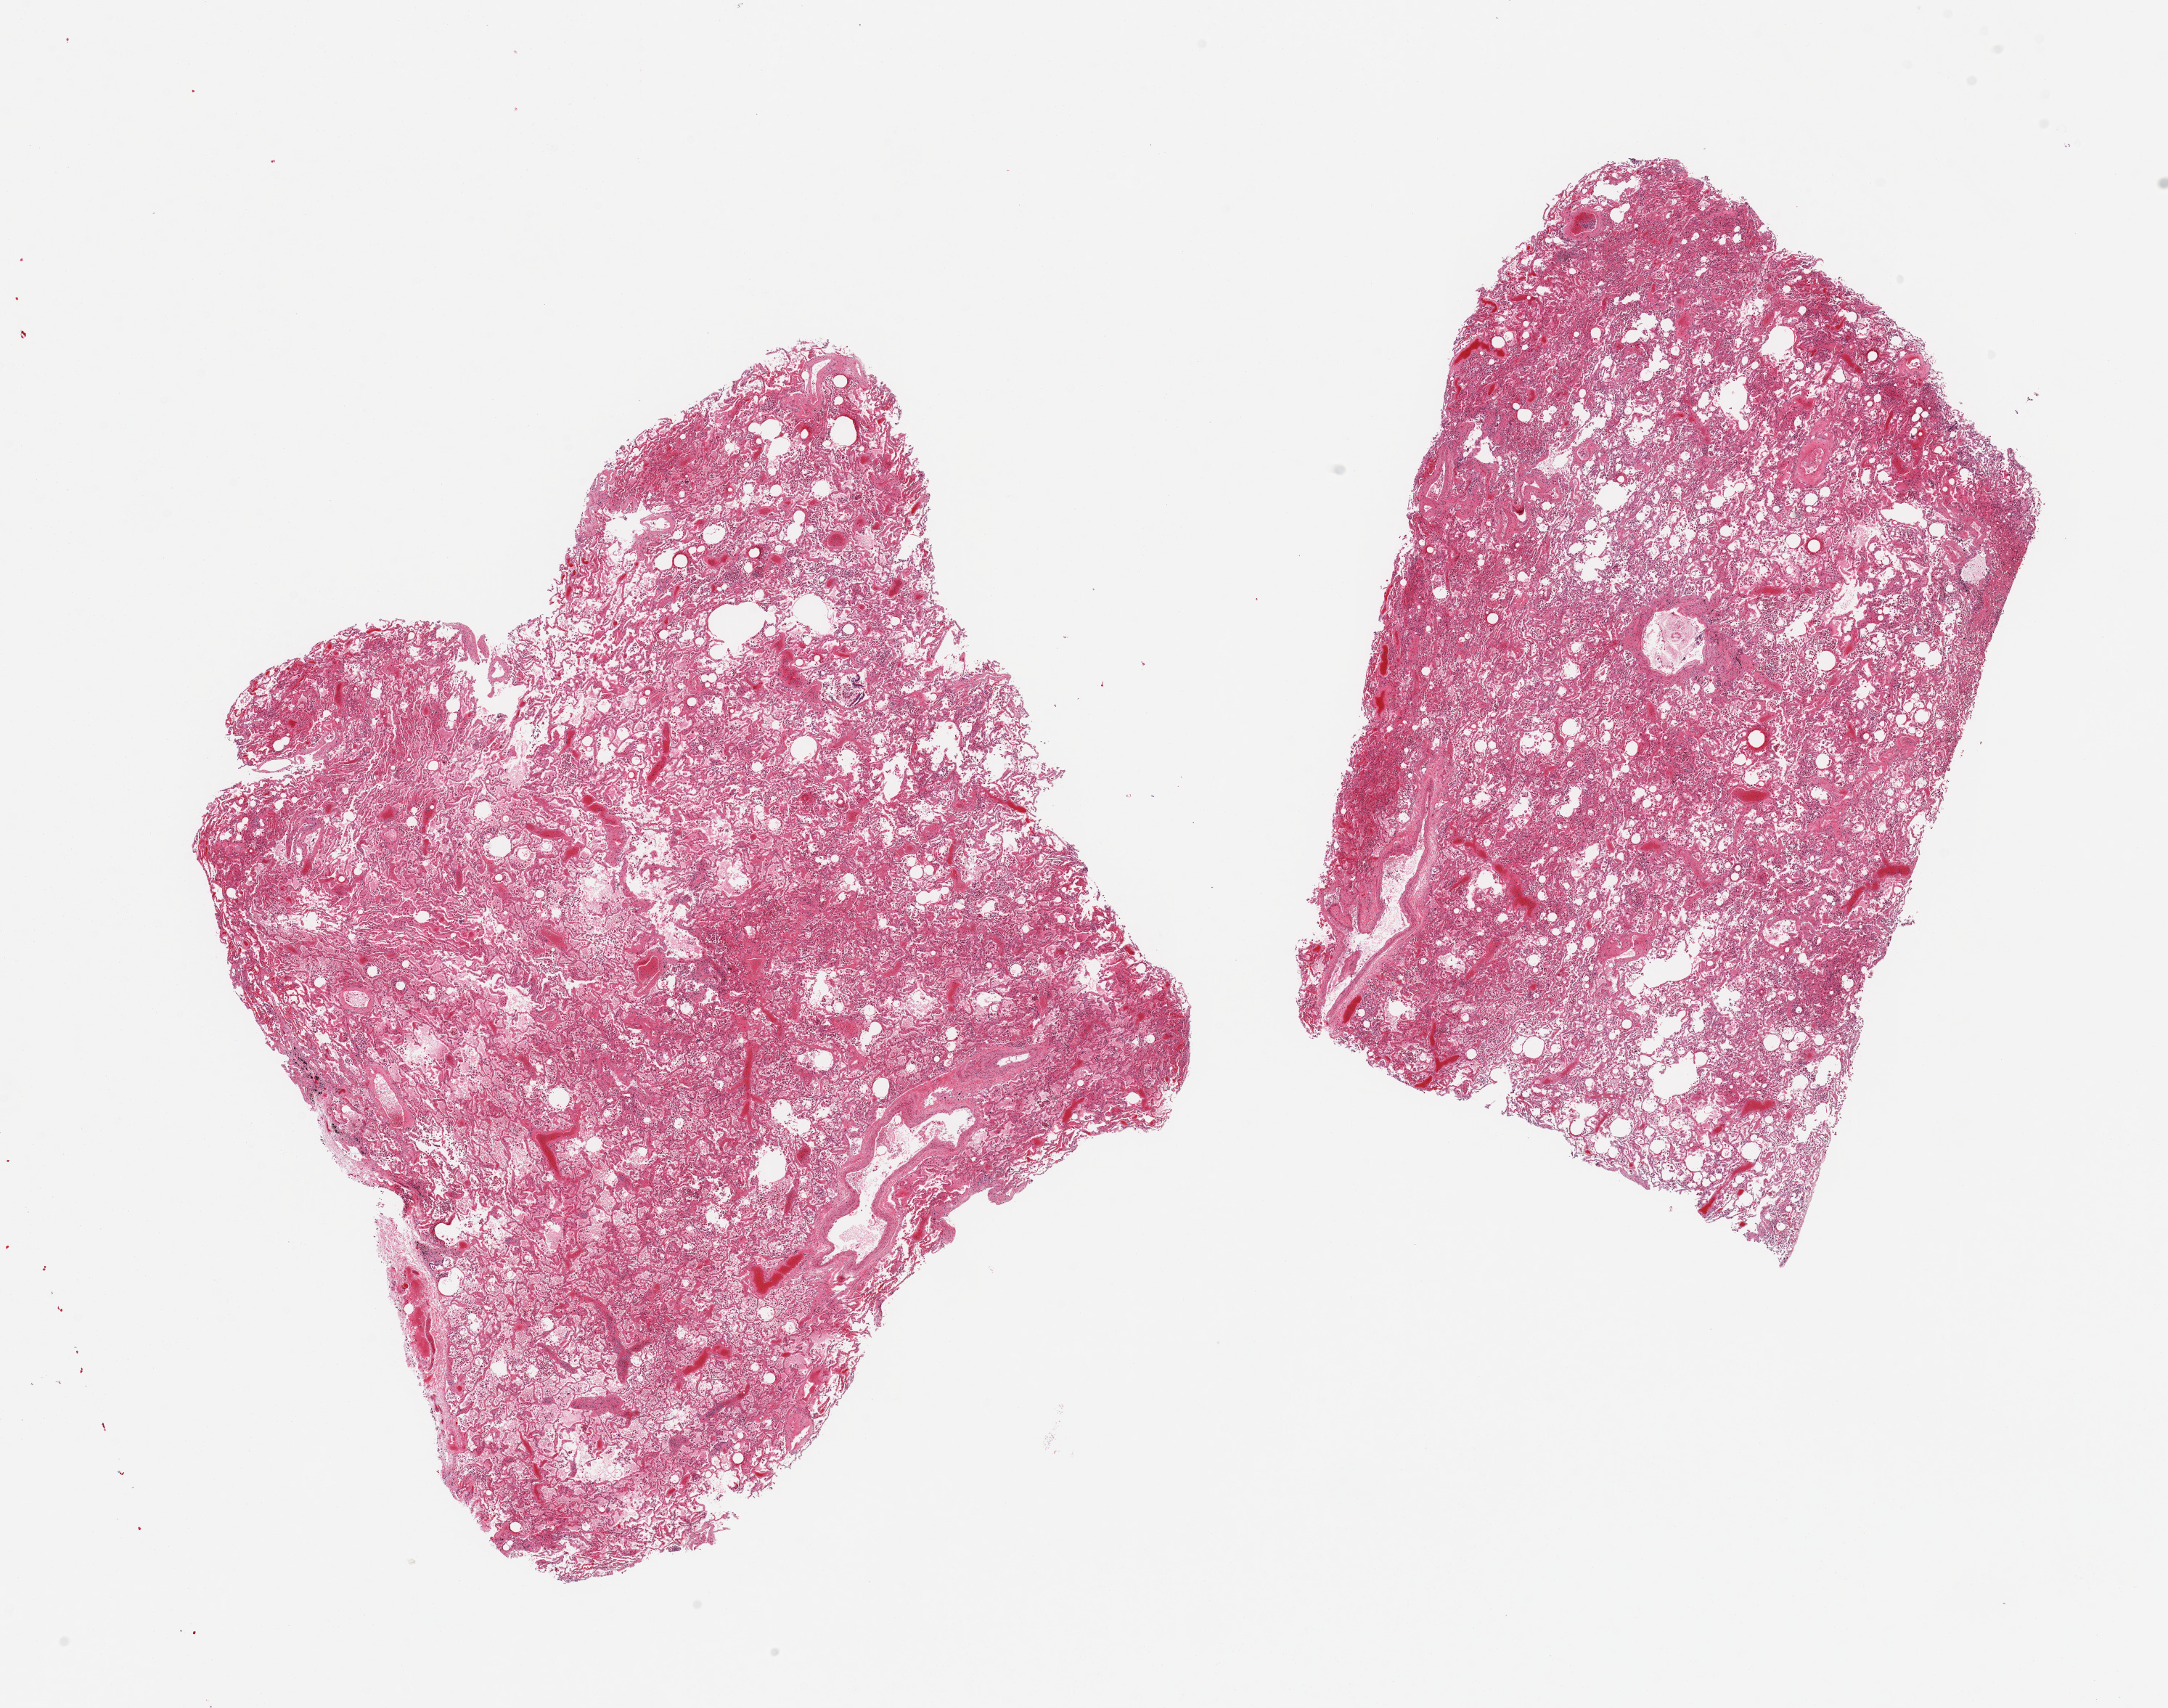
Digitized H&E-stained section, shown as a low-resolution overview of the whole scanned area (about 23.6 x 18.6 mm). PAXgene-fixed, paraffin-embedded tissue. Target tissue: lung. Tissue donor sample. Male donor.
Pathologist's review note for this sample: 2 pieces, diffuse chronic congestive changes (alveolar hemosiderin-laden macrophages), moderate-marked.